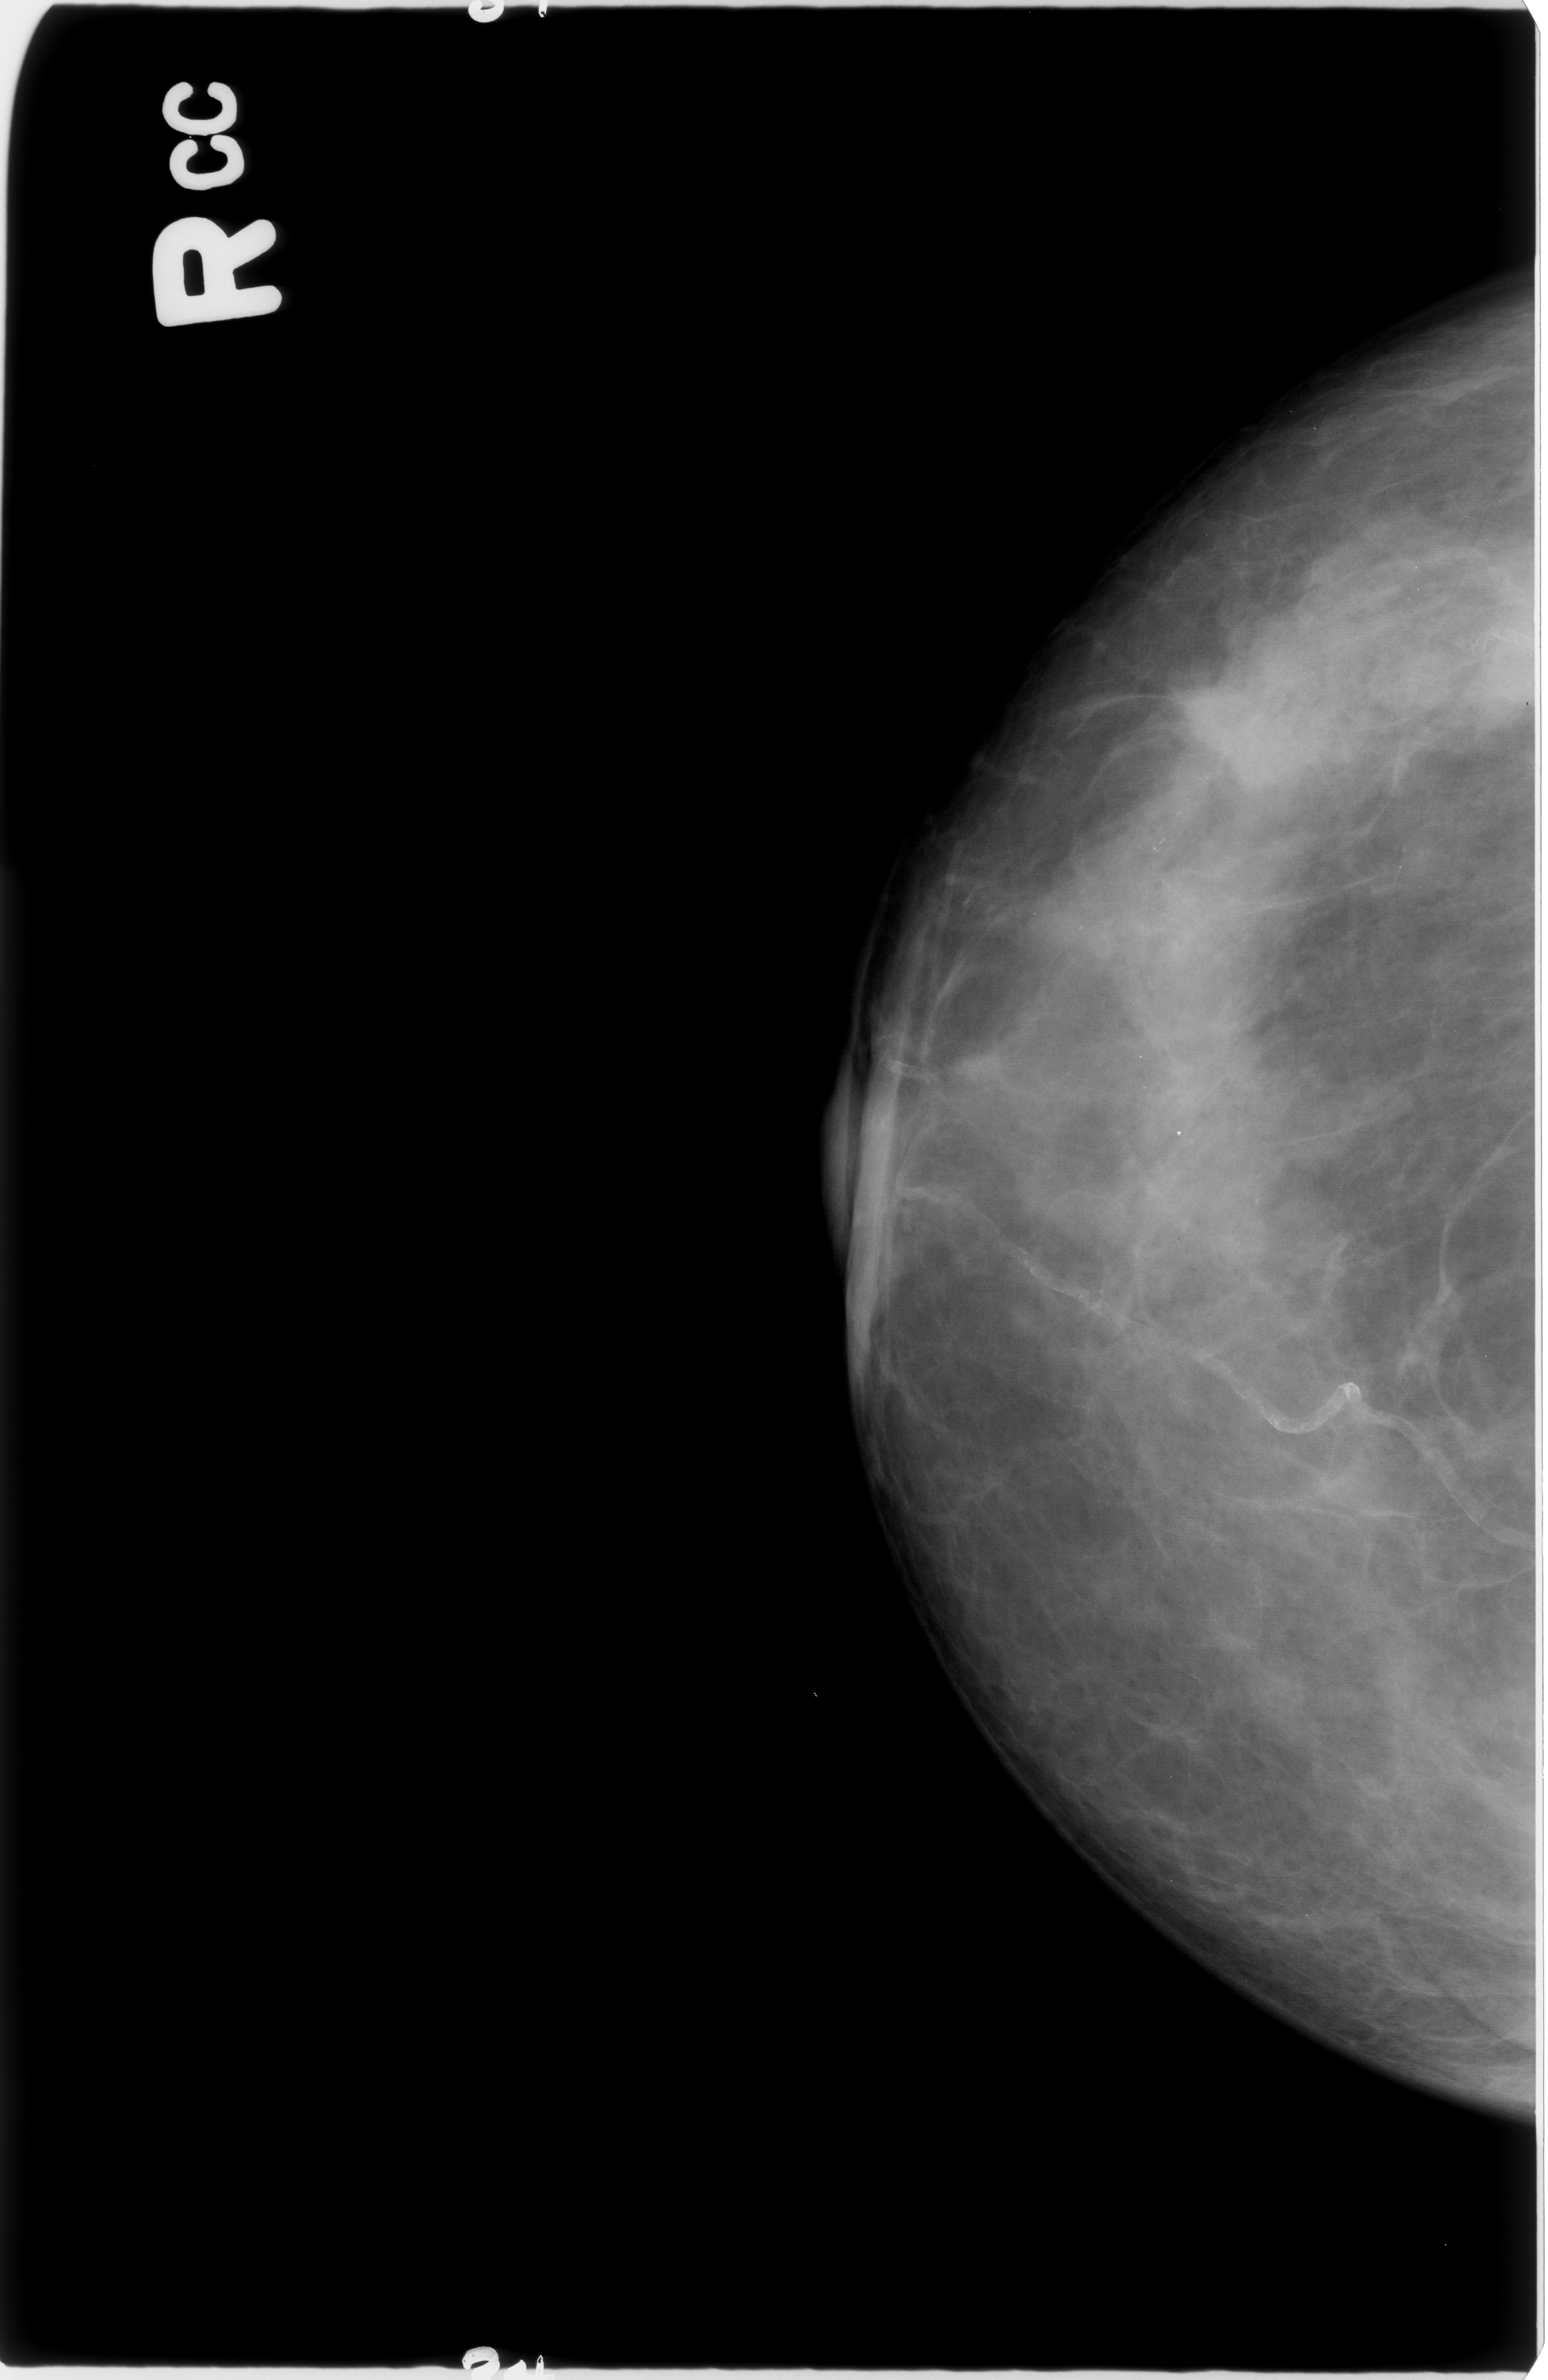
Mammogram (digitized film); right breast; craniocaudal (CC) view; breast composition: heterogeneously dense (BI-RADS density category 3 of 4); 1548 × 2380 image matrix.
Expert-marked regions of interest on this film, with their recorded descriptors:
- mass, shape irregular, margins ill defined / spiculated; BI-RADS assessment category 4; subtlety rating 3 on a 1 (subtle) to 5 (obvious) scale; pathology (as recorded): malignant: bounding box <1168,671,1316,809> (left, top, right, bottom; pixels)